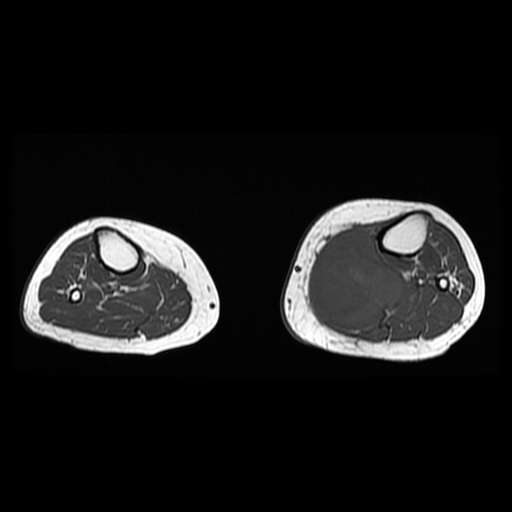
MRI of an extremity soft-tissue mass, one axial slice; position 18 of 38 along the scan axis; 512 × 512 image matrix, field of view 330 × 330 mm. Female patient. Case-level facts recorded for this patient, not image findings: histological type: extraskeletal high grade osteogenic sarcoma; grade: high; site of the primary tumour: left calf.
Structures marked on this image (expert manual segmentation):
- gross tumour volume (mass): bounding box <309,230,403,325> (left, top, right, bottom; pixels)